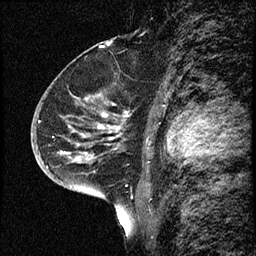
Breast MRI (dynamic contrast-enhanced), one sagittal slice; position 42 of 68 along the scan axis; dynamic contrast-enhanced study with each time point stored as its own series, time point 2 of 3 at this slice position (early post-contrast, ordered by acquisition time); 1.5 T; TE 4.2 ms, TR 17.6 ms; 2 mm slice thickness; 256 × 256 image matrix, field of view 200 × 200 mm. Patient: female, 52 years. From the clinical record (not read from this slice): setting: breast cancer imaged before/during neoadjuvant chemotherapy; receptor status: HER2-positive.
Structures marked on this image (semi-automatic segmentation, software-assisted and operator-edited):
- analysis volume of interest (the breast-tissue region the enhancement analysis was run in; not a lesion): bounding box <50,61,130,184> (left, top, right, bottom; pixels)
- tumour enhancement mask (voxels above the 100 % enhancement threshold inside the analysis volume of interest): <98,113,119,132>